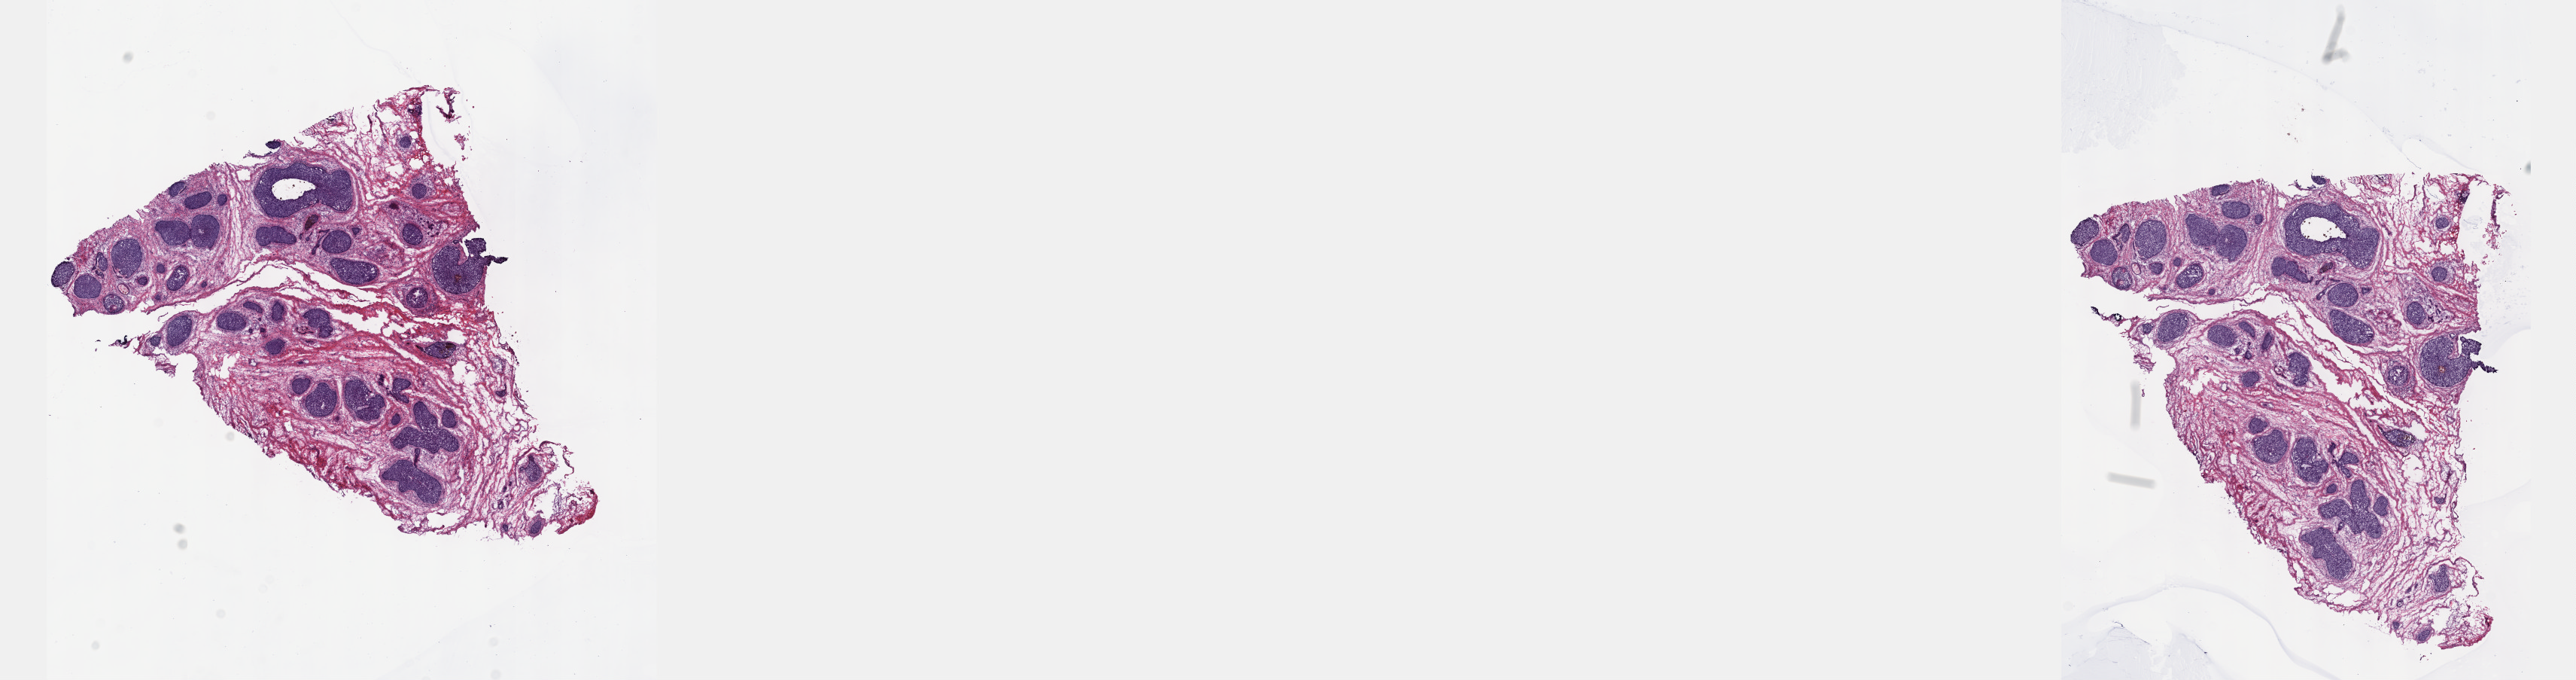
H&E-stained whole-slide image — shown as a low-resolution overview of the whole scanned area (about 27.7 x 7.3 mm), frozen section from the top of the tissue portion, sample: primary tumour, skin. Female patient. Pathologist review of this section (percent, as recorded): tumour cells 50%, tumour nuclei 75%, normal cells 50%, stromal cells 0%, necrosis 0%. Infiltration values recorded for this section: lymphocyte infiltration 0%, monocyte infiltration 0%, neutrophil infiltration 0%.
Diagnosis: Malignant melanoma, NOS. AJCC pathologic stage: II.